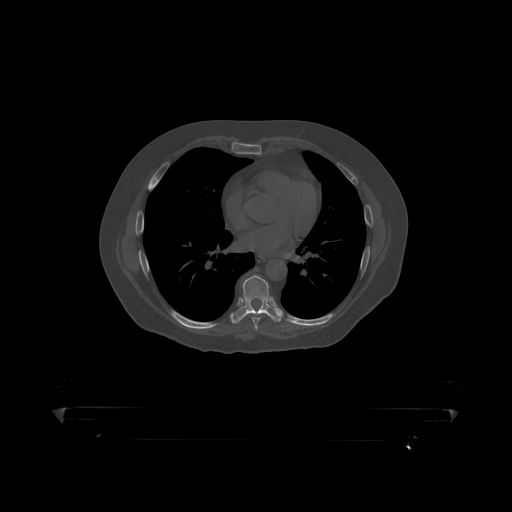
CT including the spine, one axial slice; position 264 of 390 along the scan axis; bone window (W 1800 / L 400 HU); 1.25 mm slice thickness; 512 × 512 image matrix. Patient: male, 60 years. Case-level facts recorded for this patient, not image findings: primary cancer: prostate.
Structures marked on this image (semi-automatic segmentation, software-assisted and operator-edited):
- T7 vertebra: bounding box [x1, y1, x2, y2] px = [252, 317, 260, 319]
- T8 vertebra: [232, 276, 283, 318]